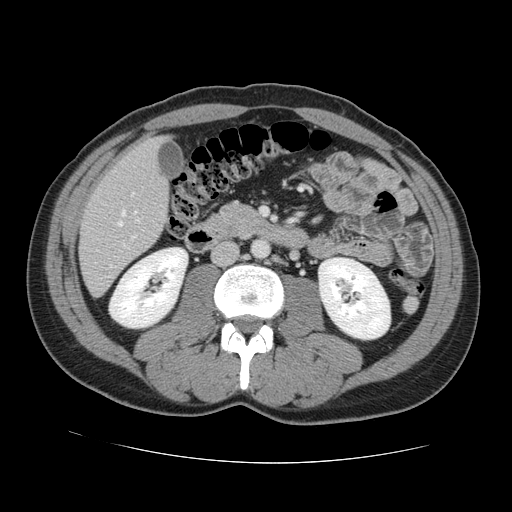
Contrast-enhanced abdominal CT, one axial slice. Slice 42 of 131 in the series (ordered by position). 120 kVp. Intravenous contrast given. Soft-tissue window (W 400 / L 40 HU). 2.5 mm slice thickness. 512 × 512 image matrix, field of view 380 × 380 mm. Male patient, age 40 years. Case-level facts recorded for this patient, not image findings: diagnosis: colorectal cancer liver metastases, imaged before liver resection; multiple liver metastases: yes; largest metastasis: 2.9 cm.
Annotated regions visible in this slice (manually delineated by an expert):
- hepatic veins: box from (x=118, y=211) to (x=139, y=226) px
- liver: (x=80, y=140)–(x=169, y=296)
- planned liver remnant (the part of the liver to remain after resection): (x=131, y=140)–(x=160, y=164)
- portal vein (with intrahepatic branches): (x=132, y=192)–(x=136, y=239)